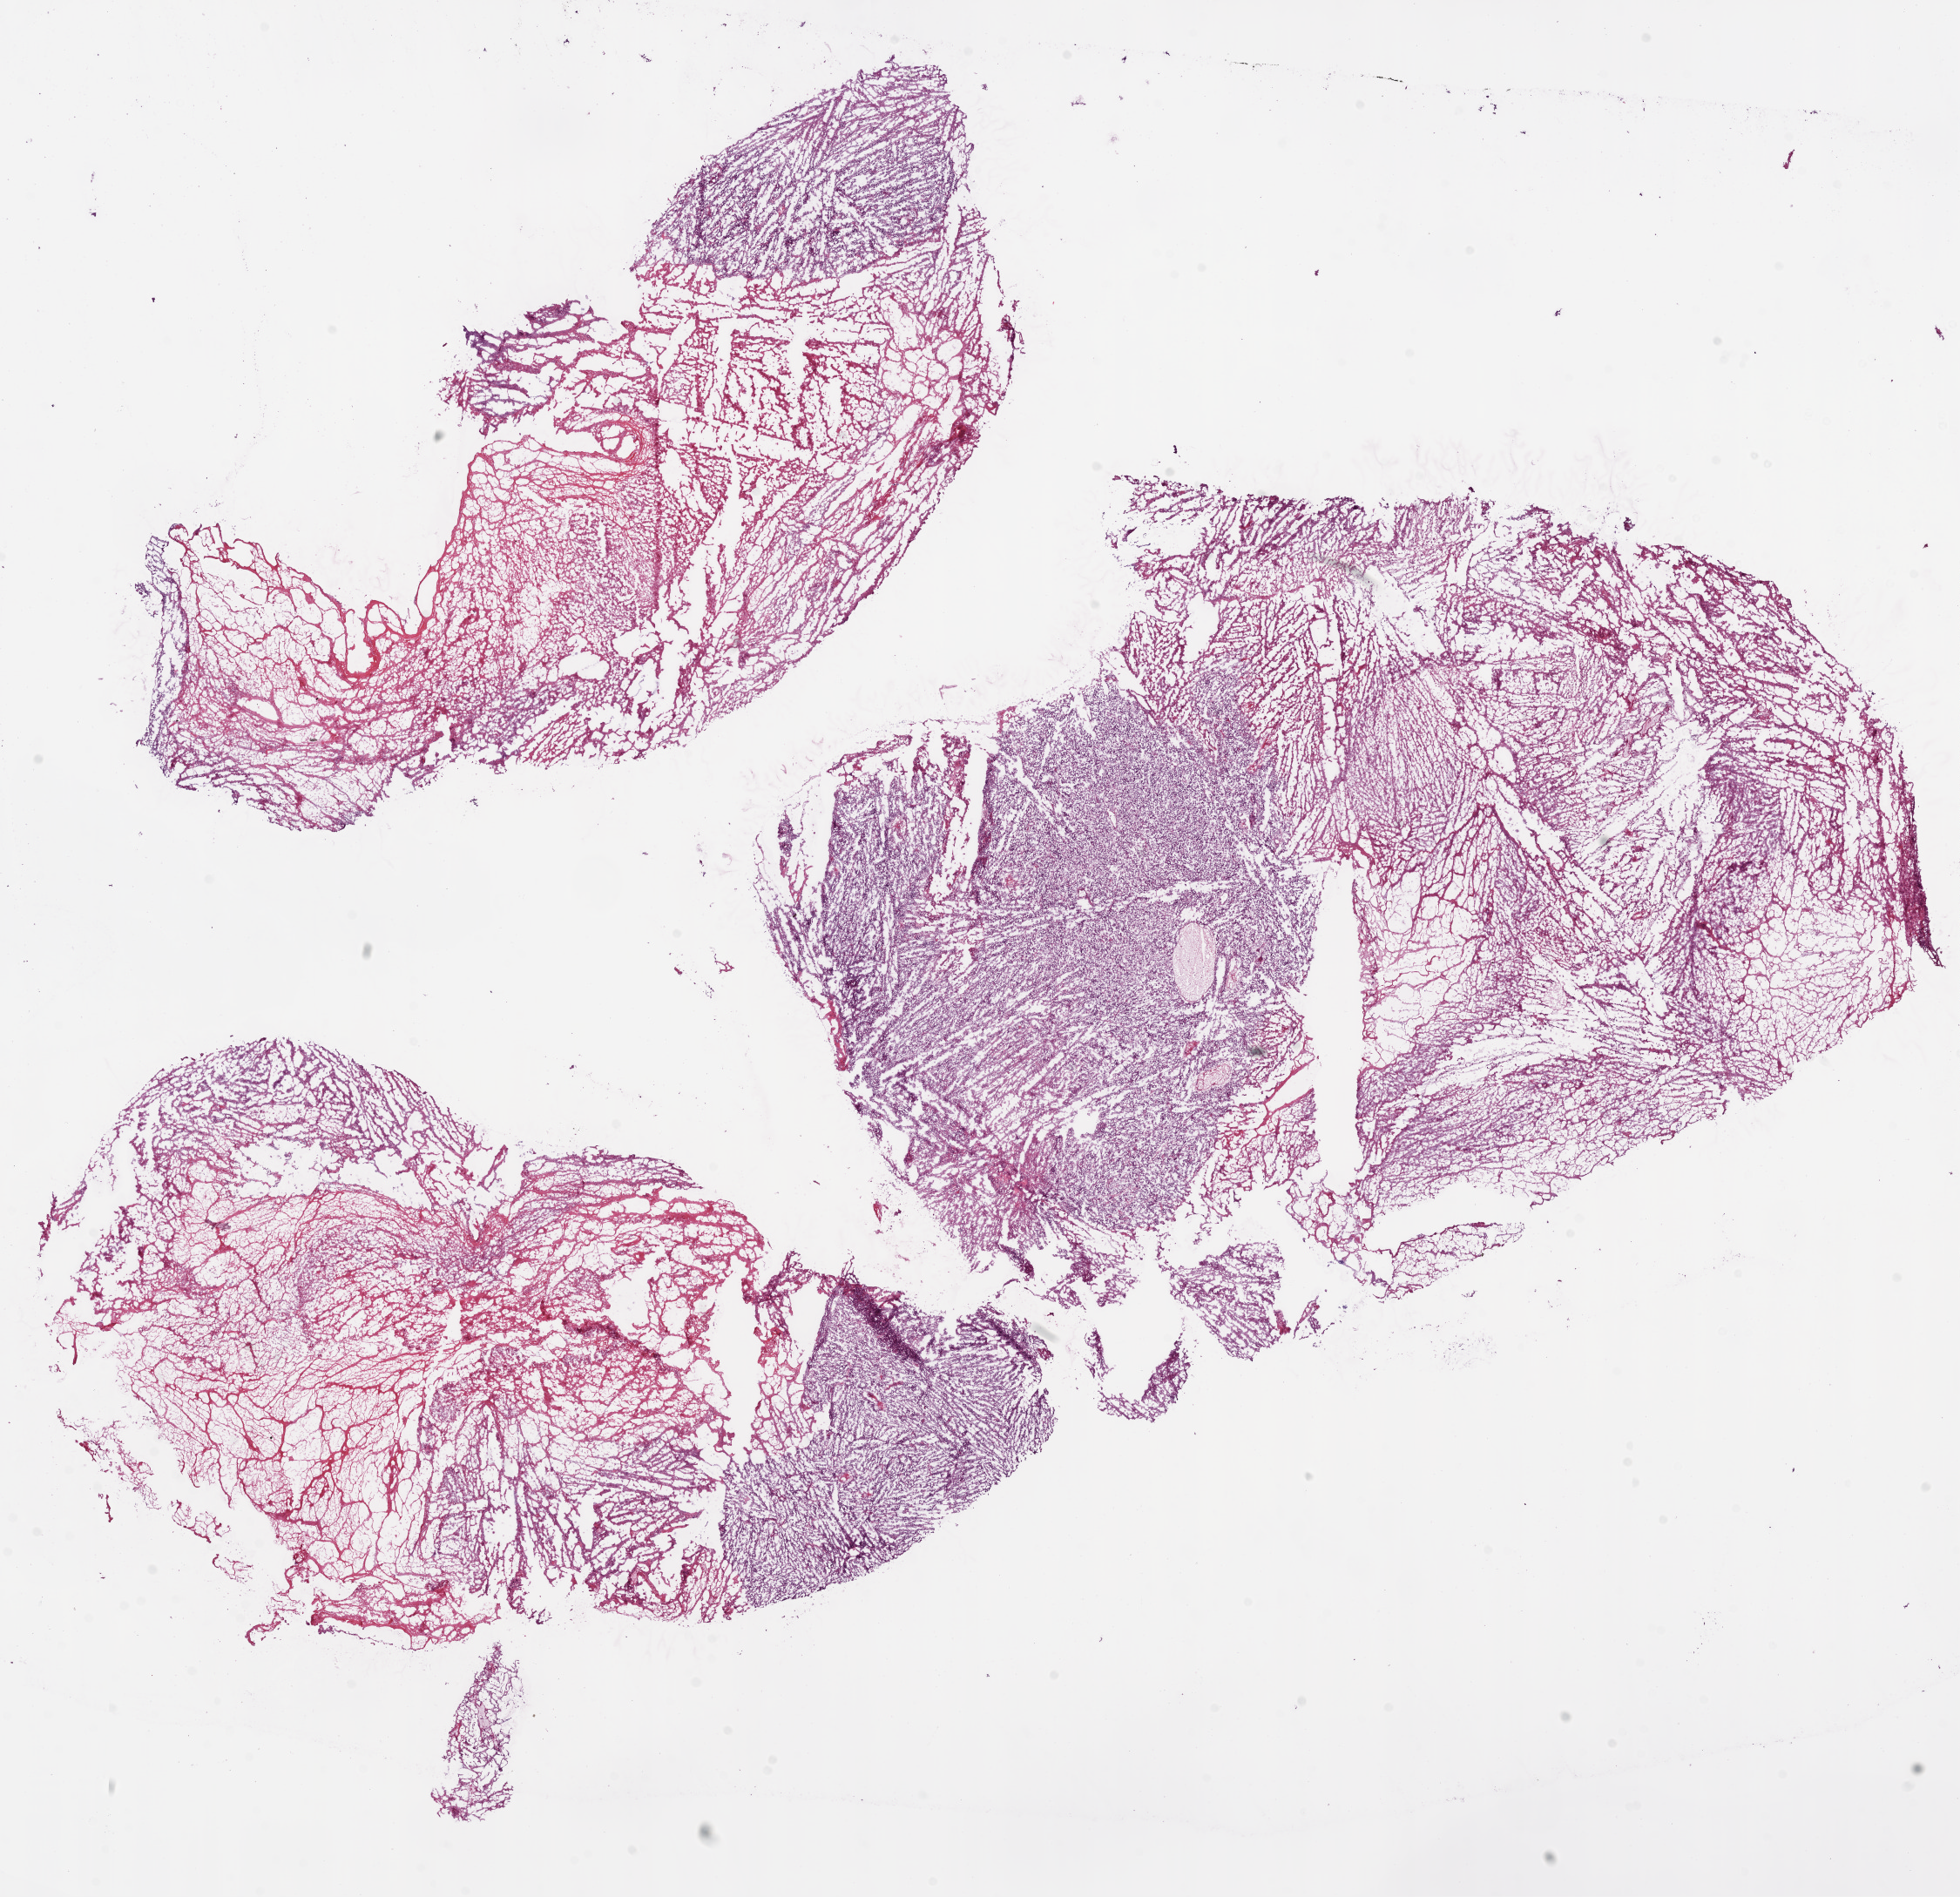
Hematoxylin and eosin (H&E) stained whole-slide image, whole scanned area (about 18.1 x 17.5 mm) shown as a low-resolution overview. Frozen section from the bottom of the tissue portion. Brain, primary tumour sample. Female patient; age at initial diagnosis 85 years. Slide review estimates, as recorded: tumour cells 50%, tumour nuclei 80%, normal cells 0%, stromal cells 0%, necrosis 50%.
Pathologic diagnosis: Glioblastoma.